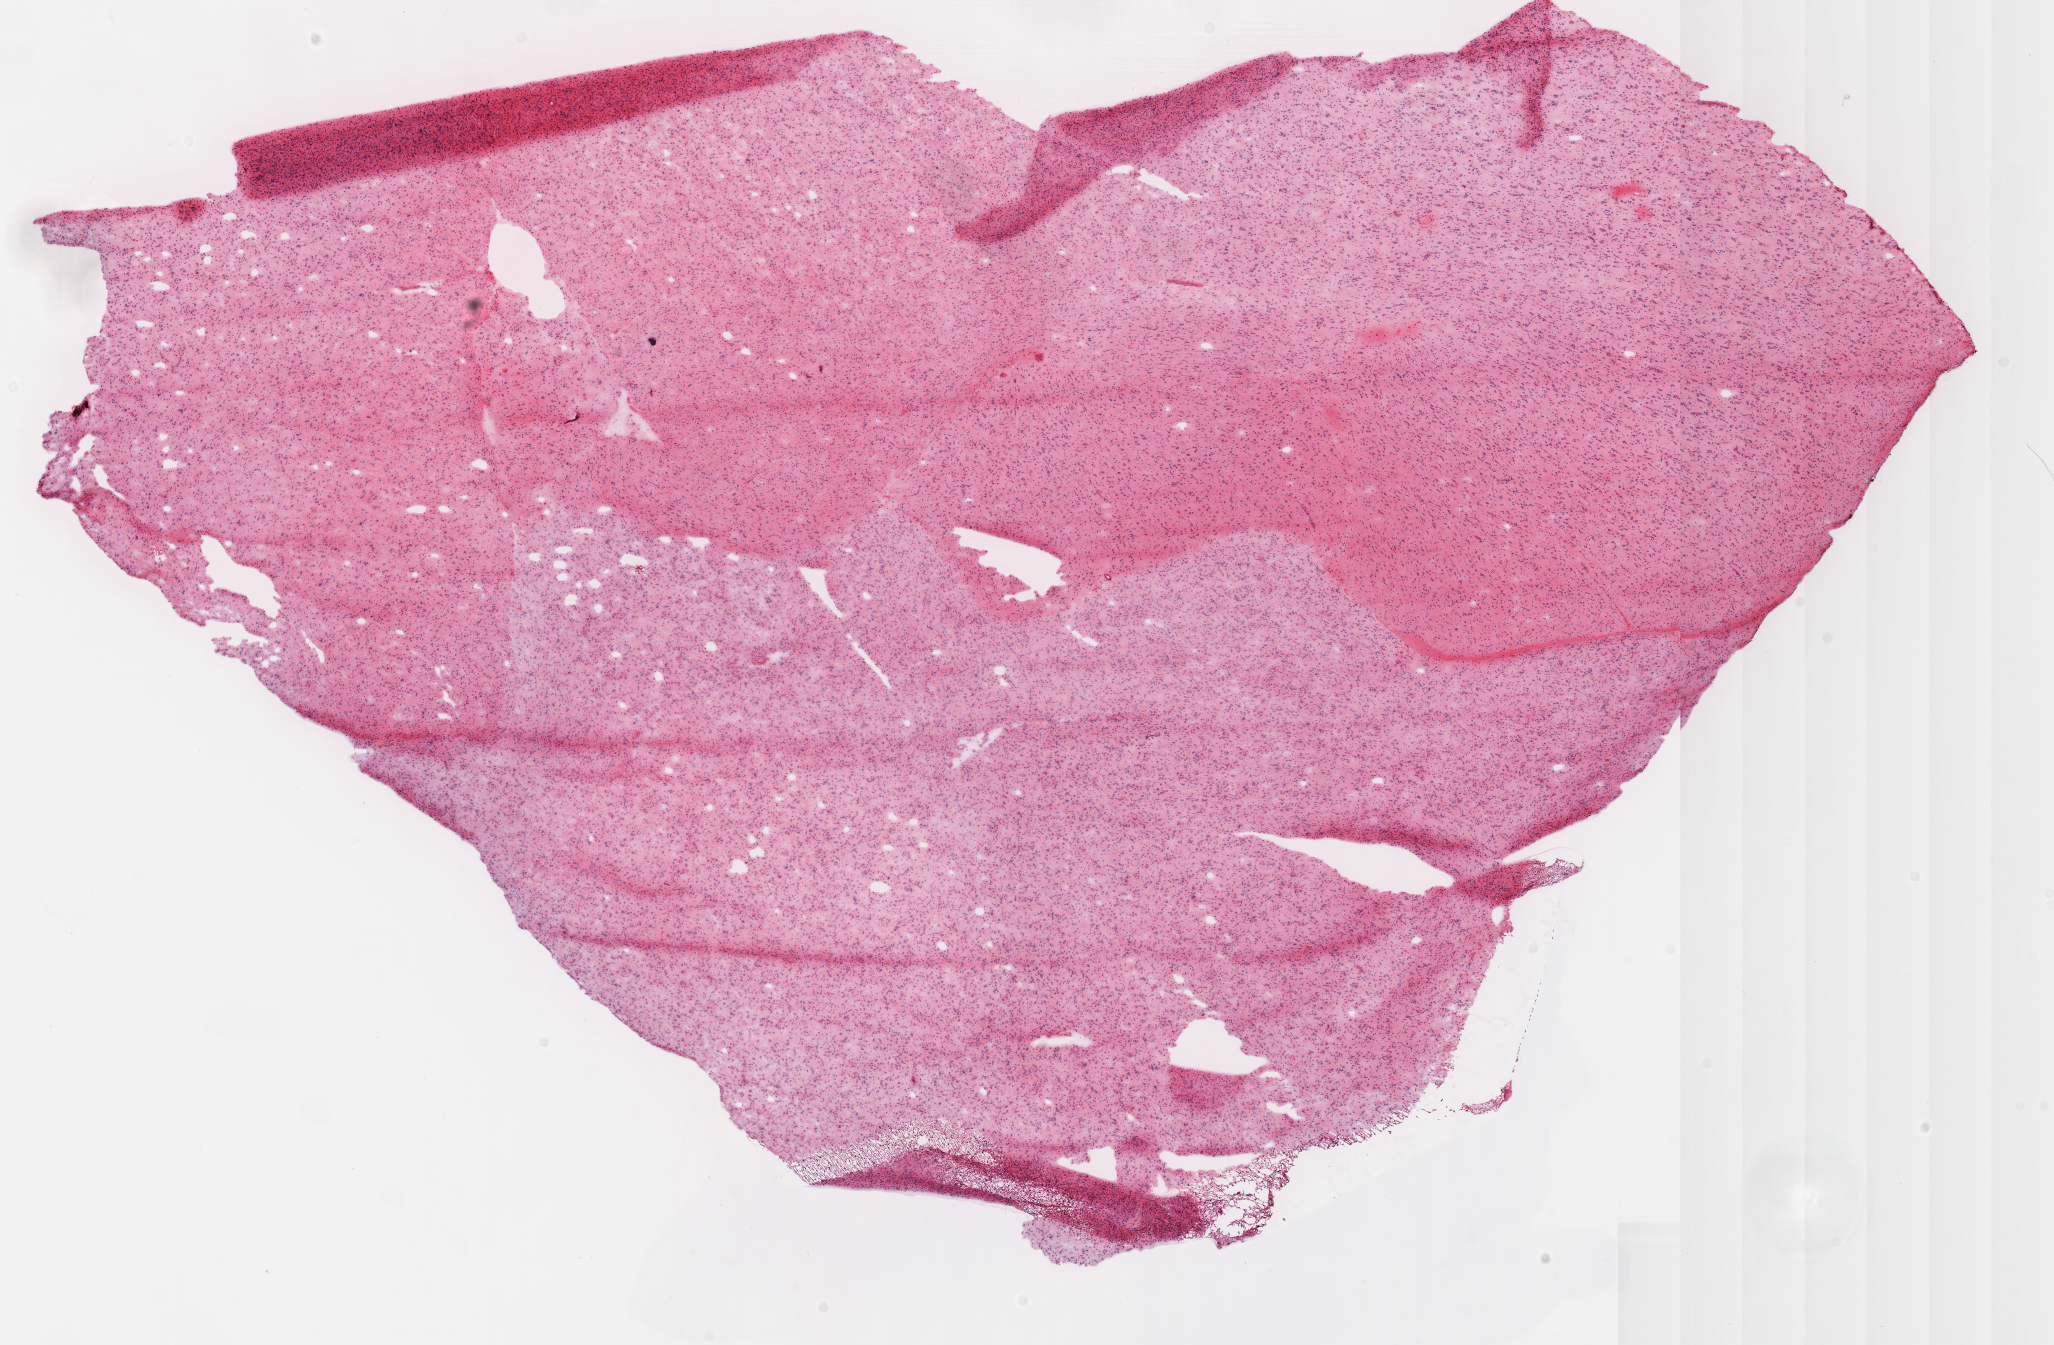
Hematoxylin and eosin (H&E) stained whole-slide image, whole scanned area (about 16.2 x 10.6 mm) shown as a low-resolution overview, frozen section from the top of the tissue portion, sample: primary tumour, brain. Female patient; age at initial diagnosis 34 years. Histologic grade: G3 (poorly differentiated). Composition of this section per pathologist review: tumour cells 100%, tumour nuclei 80%, normal cells 0%, stromal cells 0%, necrosis 0%.
Diagnosis: Astrocytoma, anaplastic.